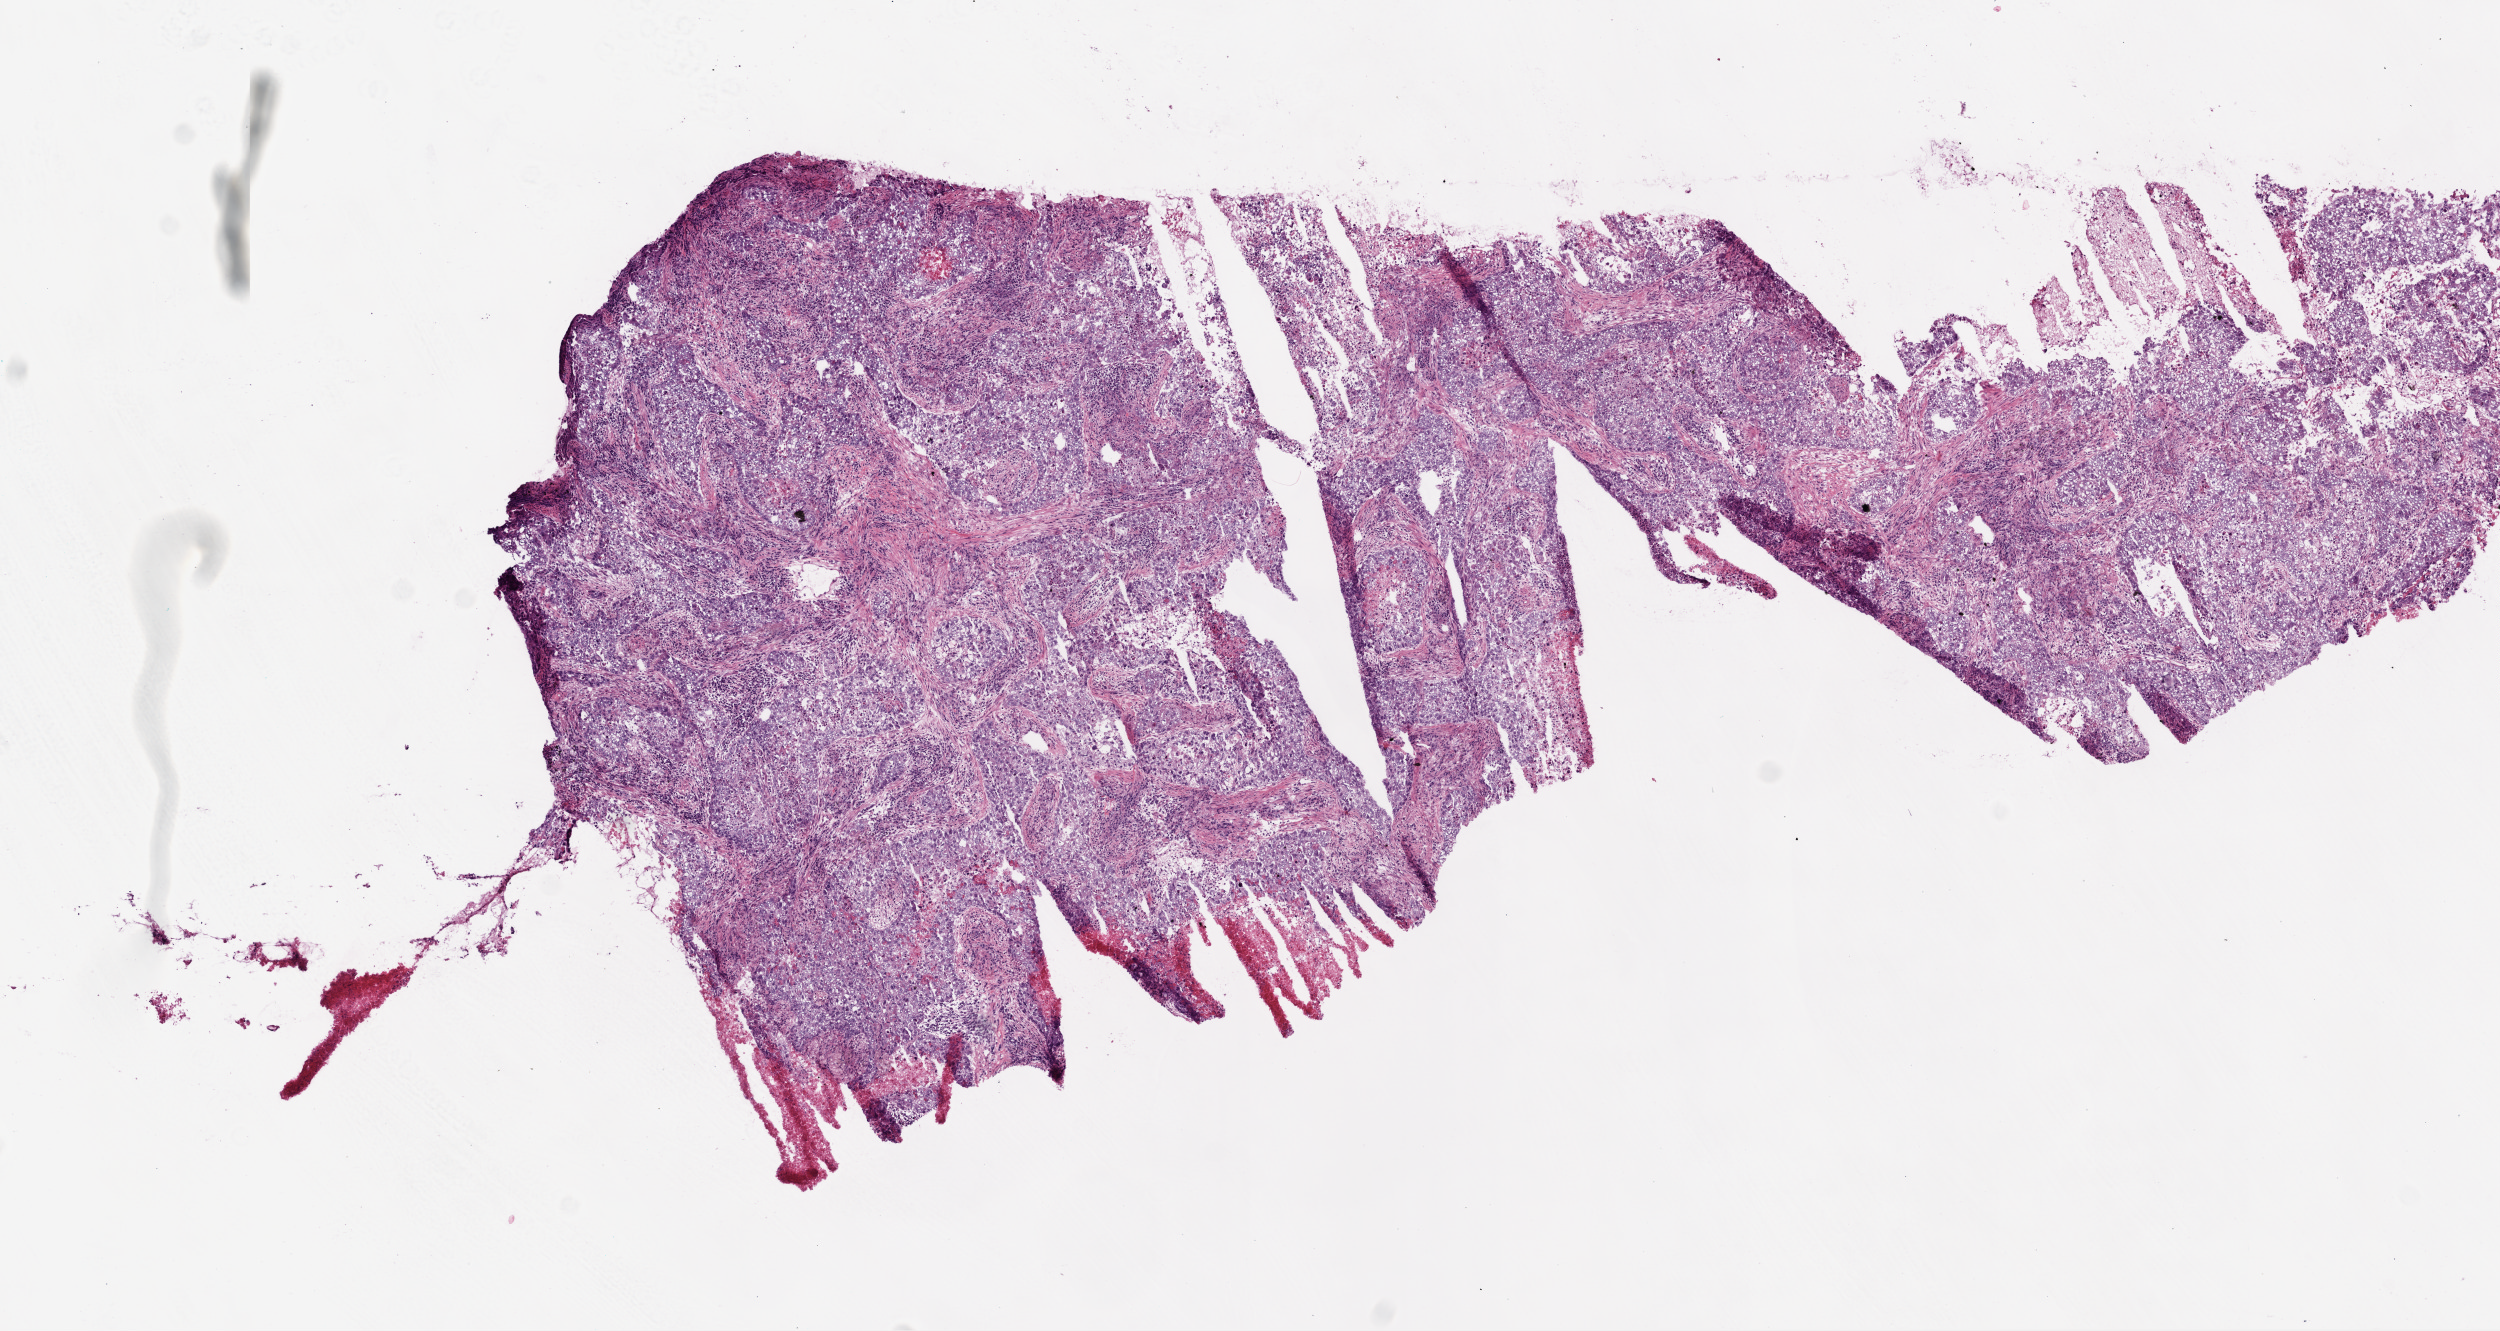
Digitized Hematoxylin and eosin (H&E) stained tissue section (whole slide), shown as a low-resolution overview of the whole scanned area (about 10.0 x 5.3 mm, acquisition: 20x scan). Frozen section from the bottom of the tissue portion. Lung, primary tumour sample. Patient: female, age at initial diagnosis 72 years. Composition of this section per pathologist review: tumour cells 82%, tumour nuclei 80%, normal cells 0%, stromal cells 5%, necrosis 8%.
AJCC pathologic stage: IB. Histologic diagnosis: Adenocarcinoma, NOS (upper lobe, lung). TNM: T2 N0 M0. Laterality: left.